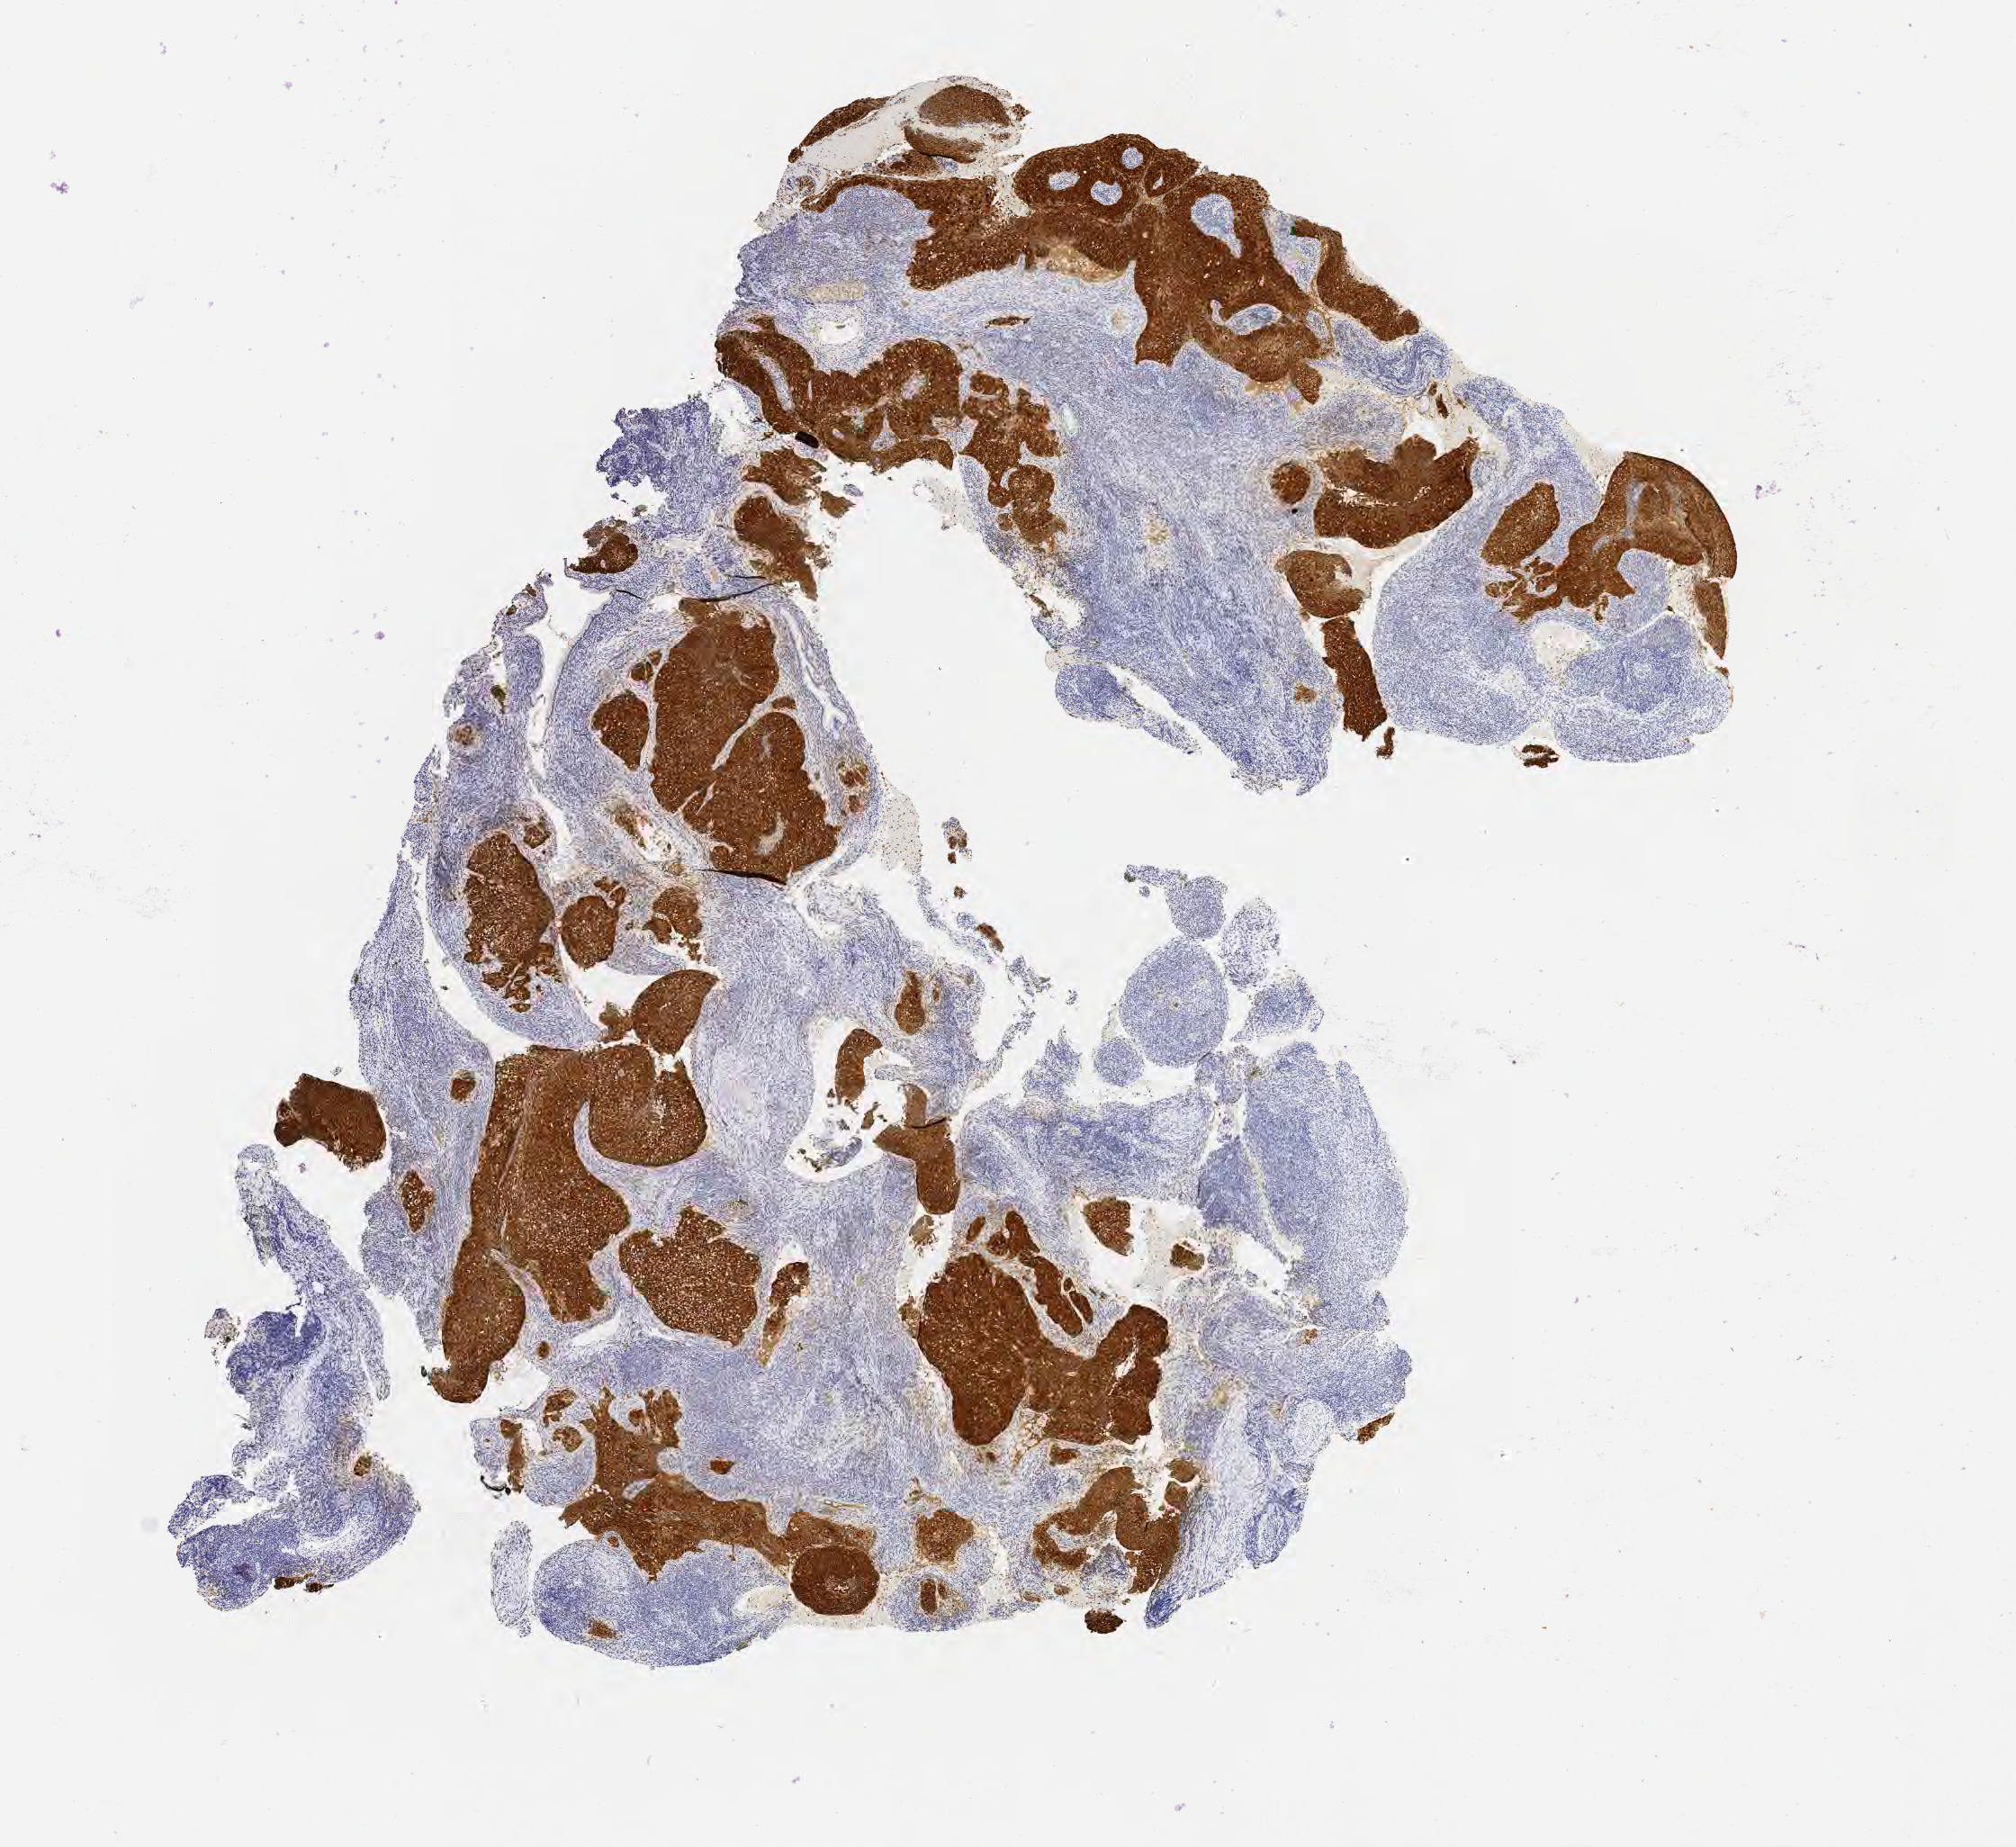
IHC for p16 (p16INK4a), whole-slide image, low-resolution overview of the scanned area, about 9.1 x 8.3 mm; specimen: tumor tissue; site: cervix. Female patient, age 50 years.
Histologic diagnosis: Squamous cell carcinoma, large cell, nonkeratinizing, NOS.